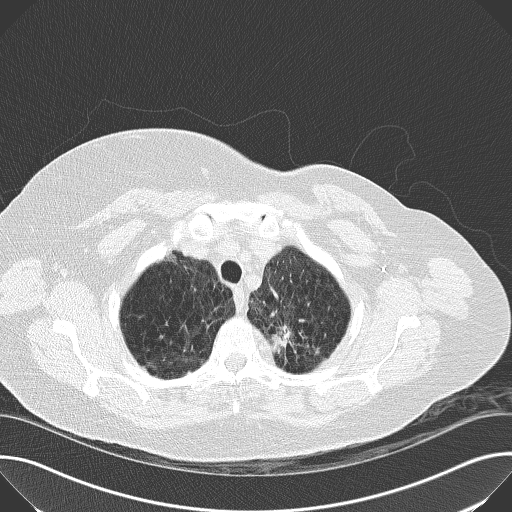
Low-dose screening chest CT, one axial slice; position 146 of 169 along the scan axis; reconstruction kernel B50f; 120 kVp; lung window (W 1500 / L -600 HU); 512 × 512 image matrix.
Structures marked on this image (expert manual segmentation):
- lesion 1 (tumor, upper lobe of left lung): bounding box <271,325,291,353> (left, top, right, bottom; pixels)